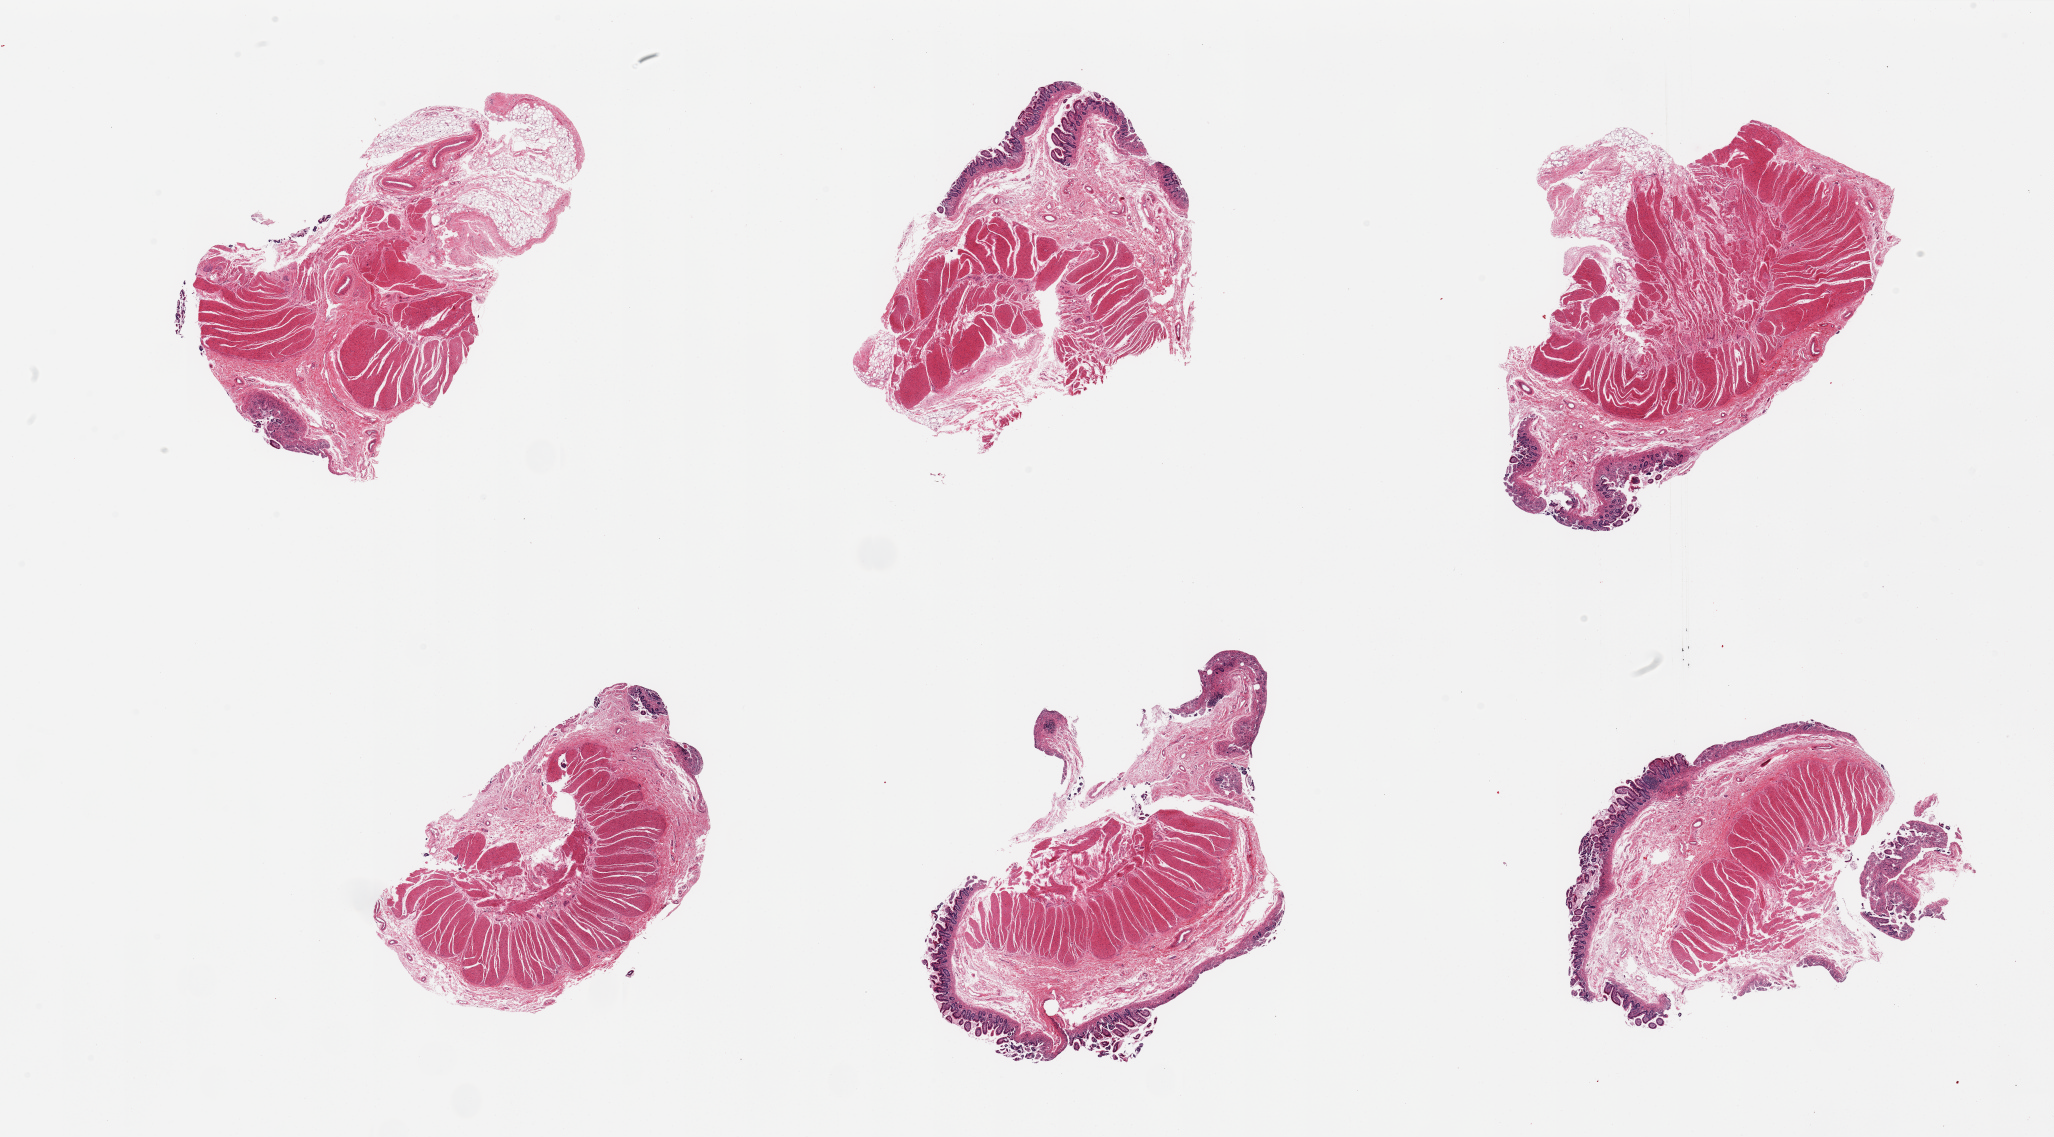
Digitized haematoxylin and eosin-stained section, a low-resolution overview of the entire scanned area, about 32.5 x 18.0 mm.
Specimen: PAXgene-fixed, paraffin-embedded tissue; sampled site (target tissue): ileum; donor tissue sample.